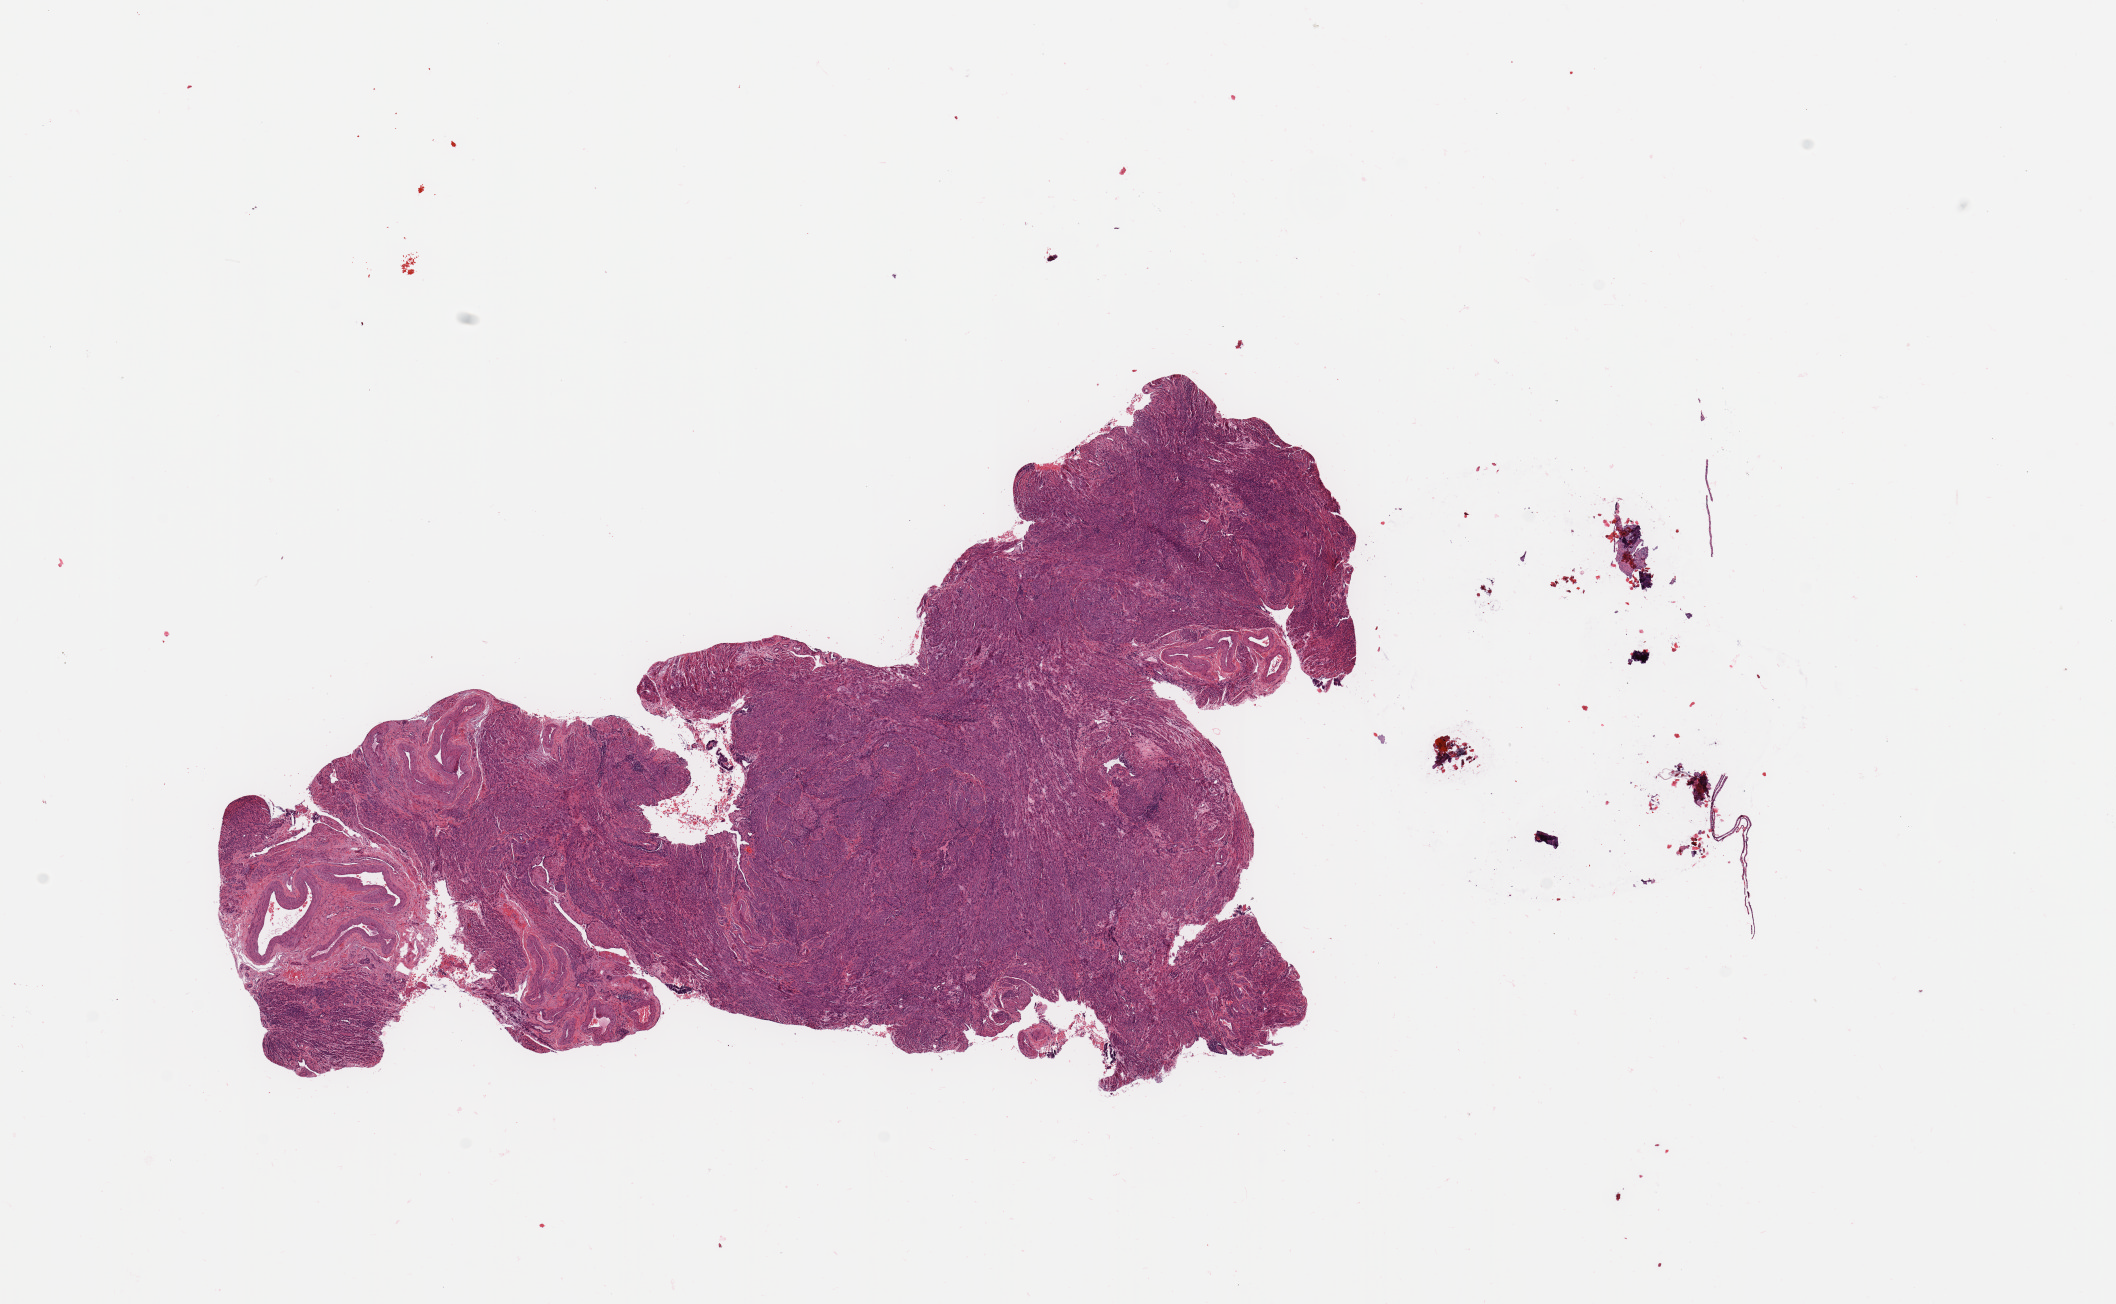
H&E-stained whole-slide image — shown as a low-resolution overview of the whole scanned area (about 16.7 x 10.3 mm, acquisition: 20x scan); uterus, tumour tissue. 65-year-old female patient. Histologic grade: G1 (well differentiated).
Histologic diagnosis: Endometrioid adenocarcinoma, NOS. AJCC pathologic stage: I.